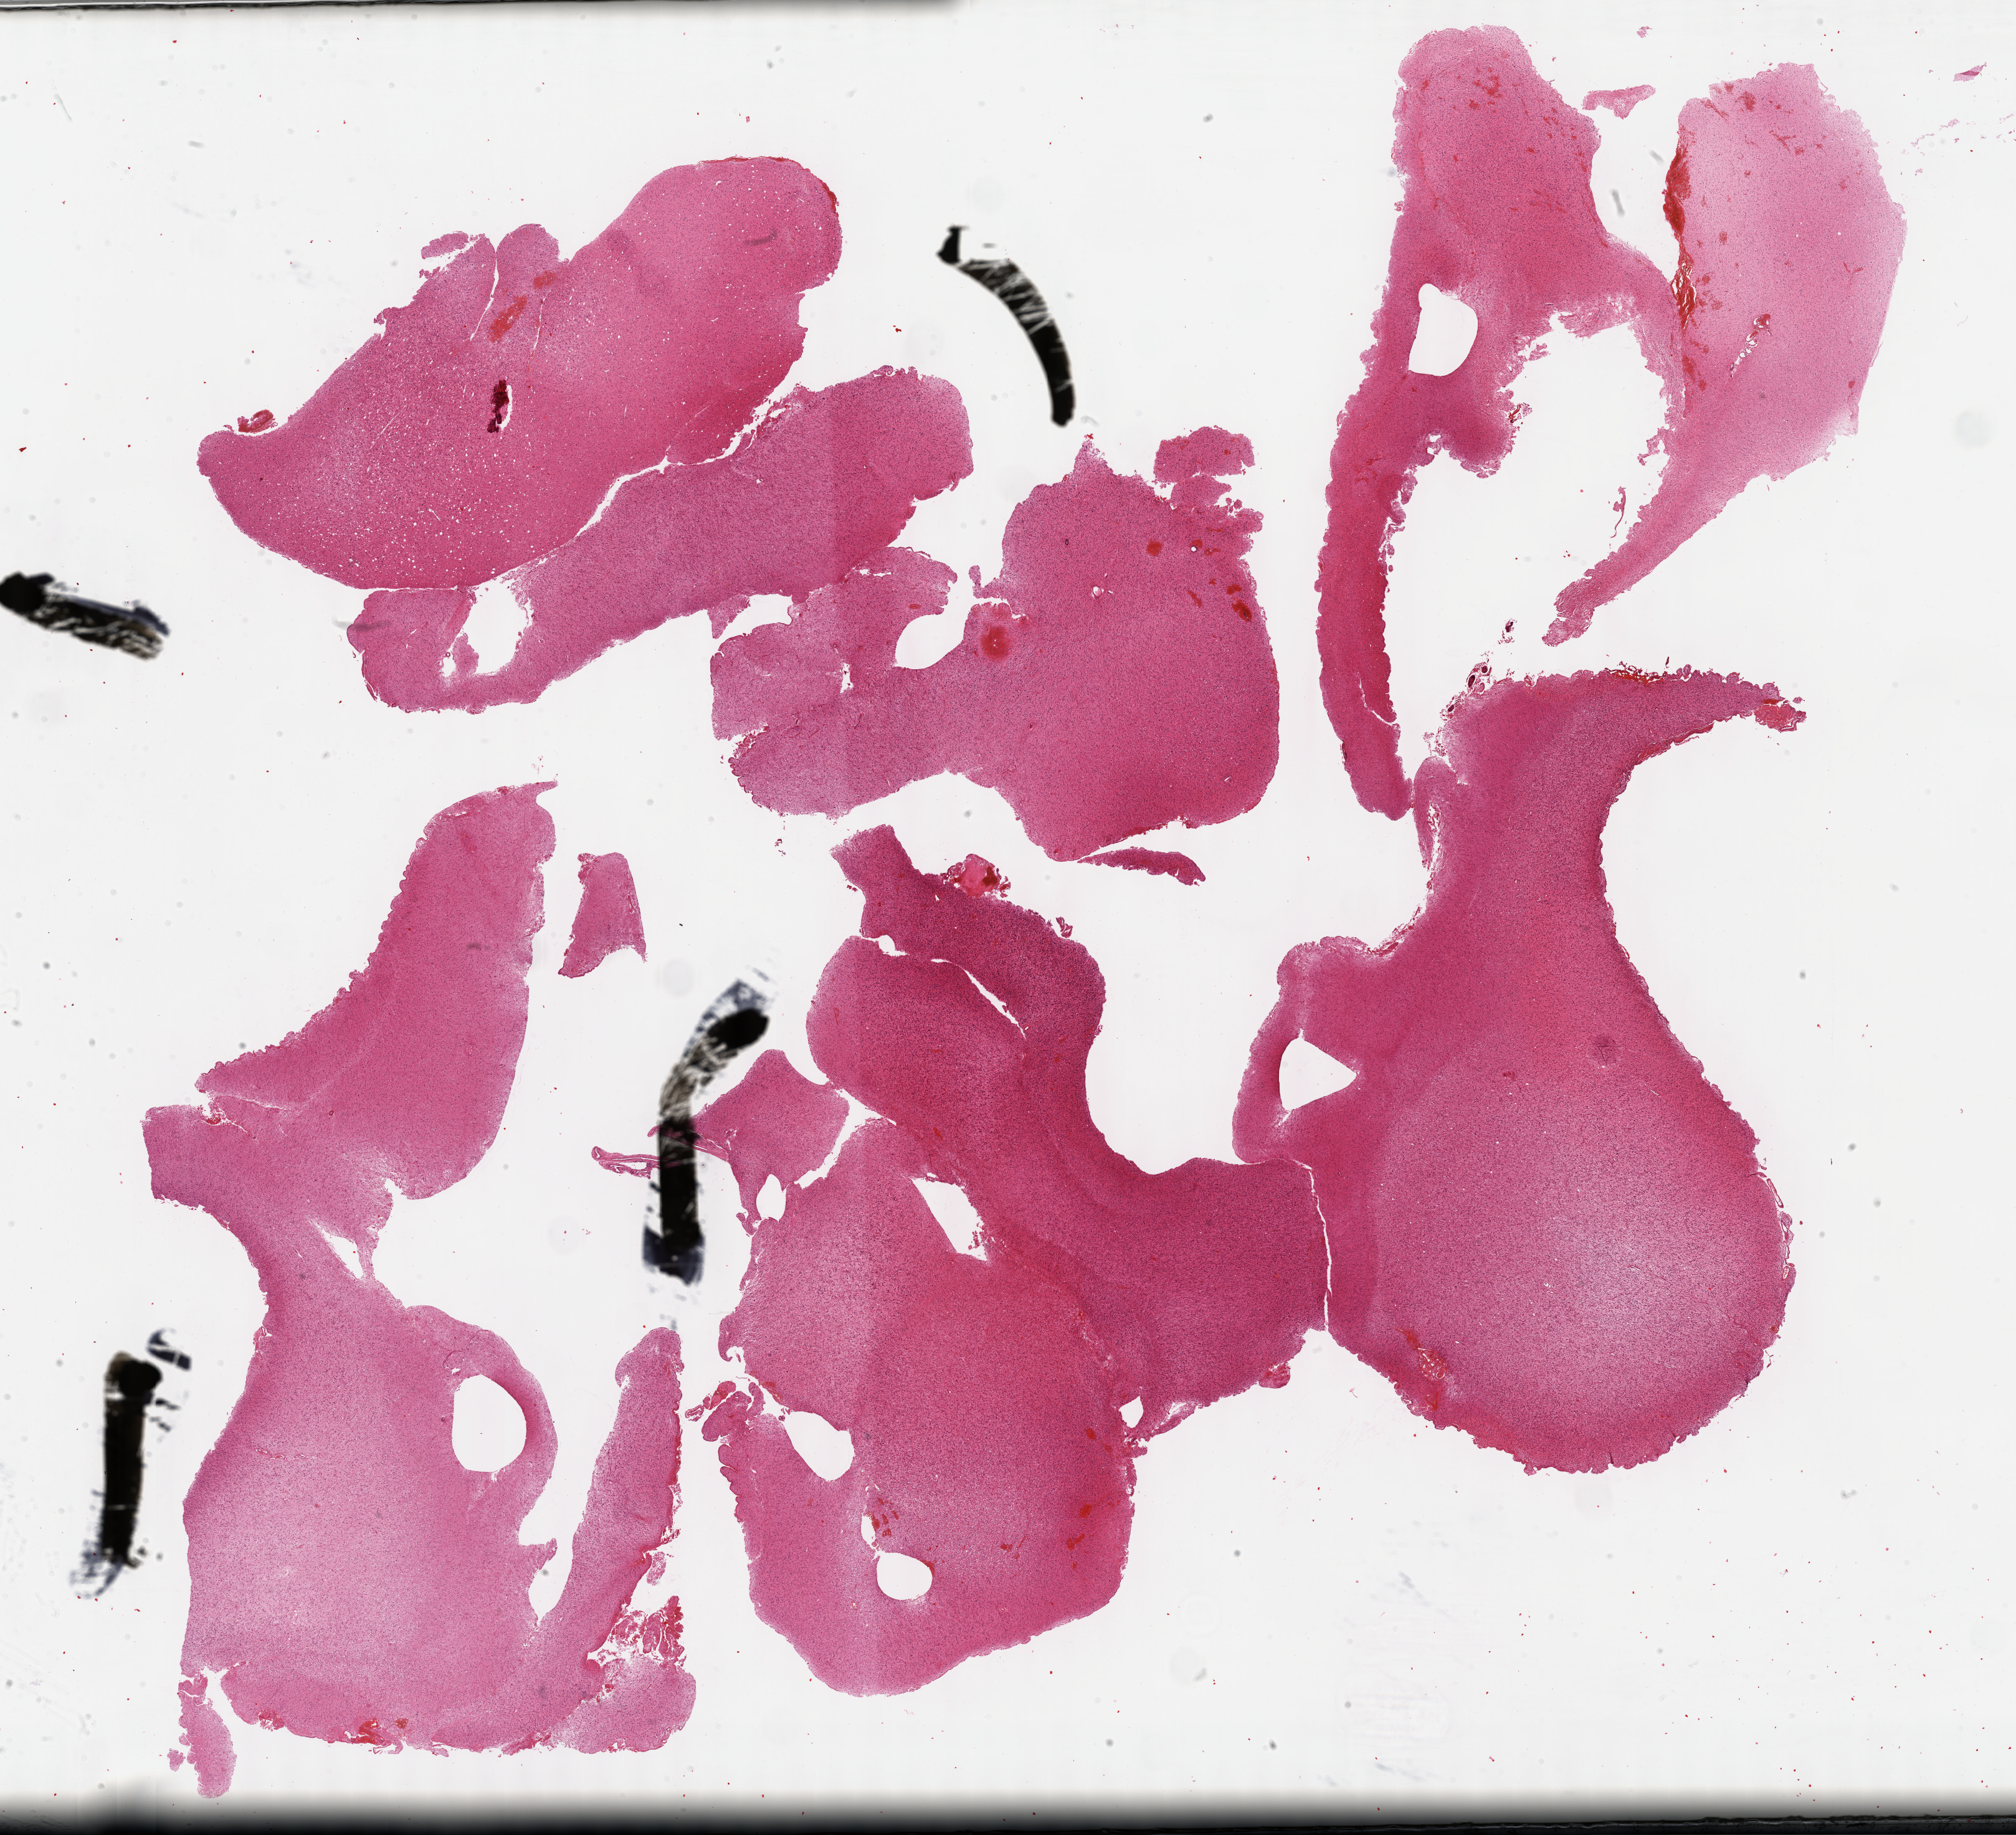
Hematoxylin and eosin (H&E) stained whole-slide image, whole scanned area (about 26.2 x 23.8 mm, from a 40x scan) shown as a low-resolution overview, FFPE section, brain, primary tumour sample. Female patient; age at initial diagnosis 36 years. Histologic grade: G3 (poorly differentiated).
Pathologic diagnosis: Astrocytoma, anaplastic (cerebrum). Laterality: right.